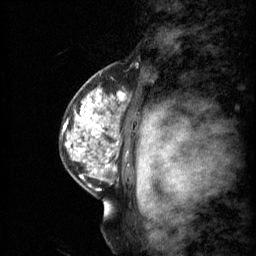
Breast MRI (dynamic contrast-enhanced), one sagittal slice; slice 44 of 60 in the series (ordered by position); 3 images stored at this slice position (order not interpretable as contrast timing); 1.5 T; TE 4.2 ms, TR 11 ms; 256 × 256 image matrix, field of view 200 × 200 mm. Patient: female, 48 years.
Structures marked on this image (semi-automatic segmentation, software-assisted and operator-edited):
- analysis volume of interest (the breast-tissue region the enhancement analysis was run in; not a lesion): box from (x=69, y=74) to (x=140, y=147) px
- tumour enhancement mask (voxels above the 70 % enhancement threshold inside the analysis volume of interest): (x=81, y=90)–(x=126, y=137)